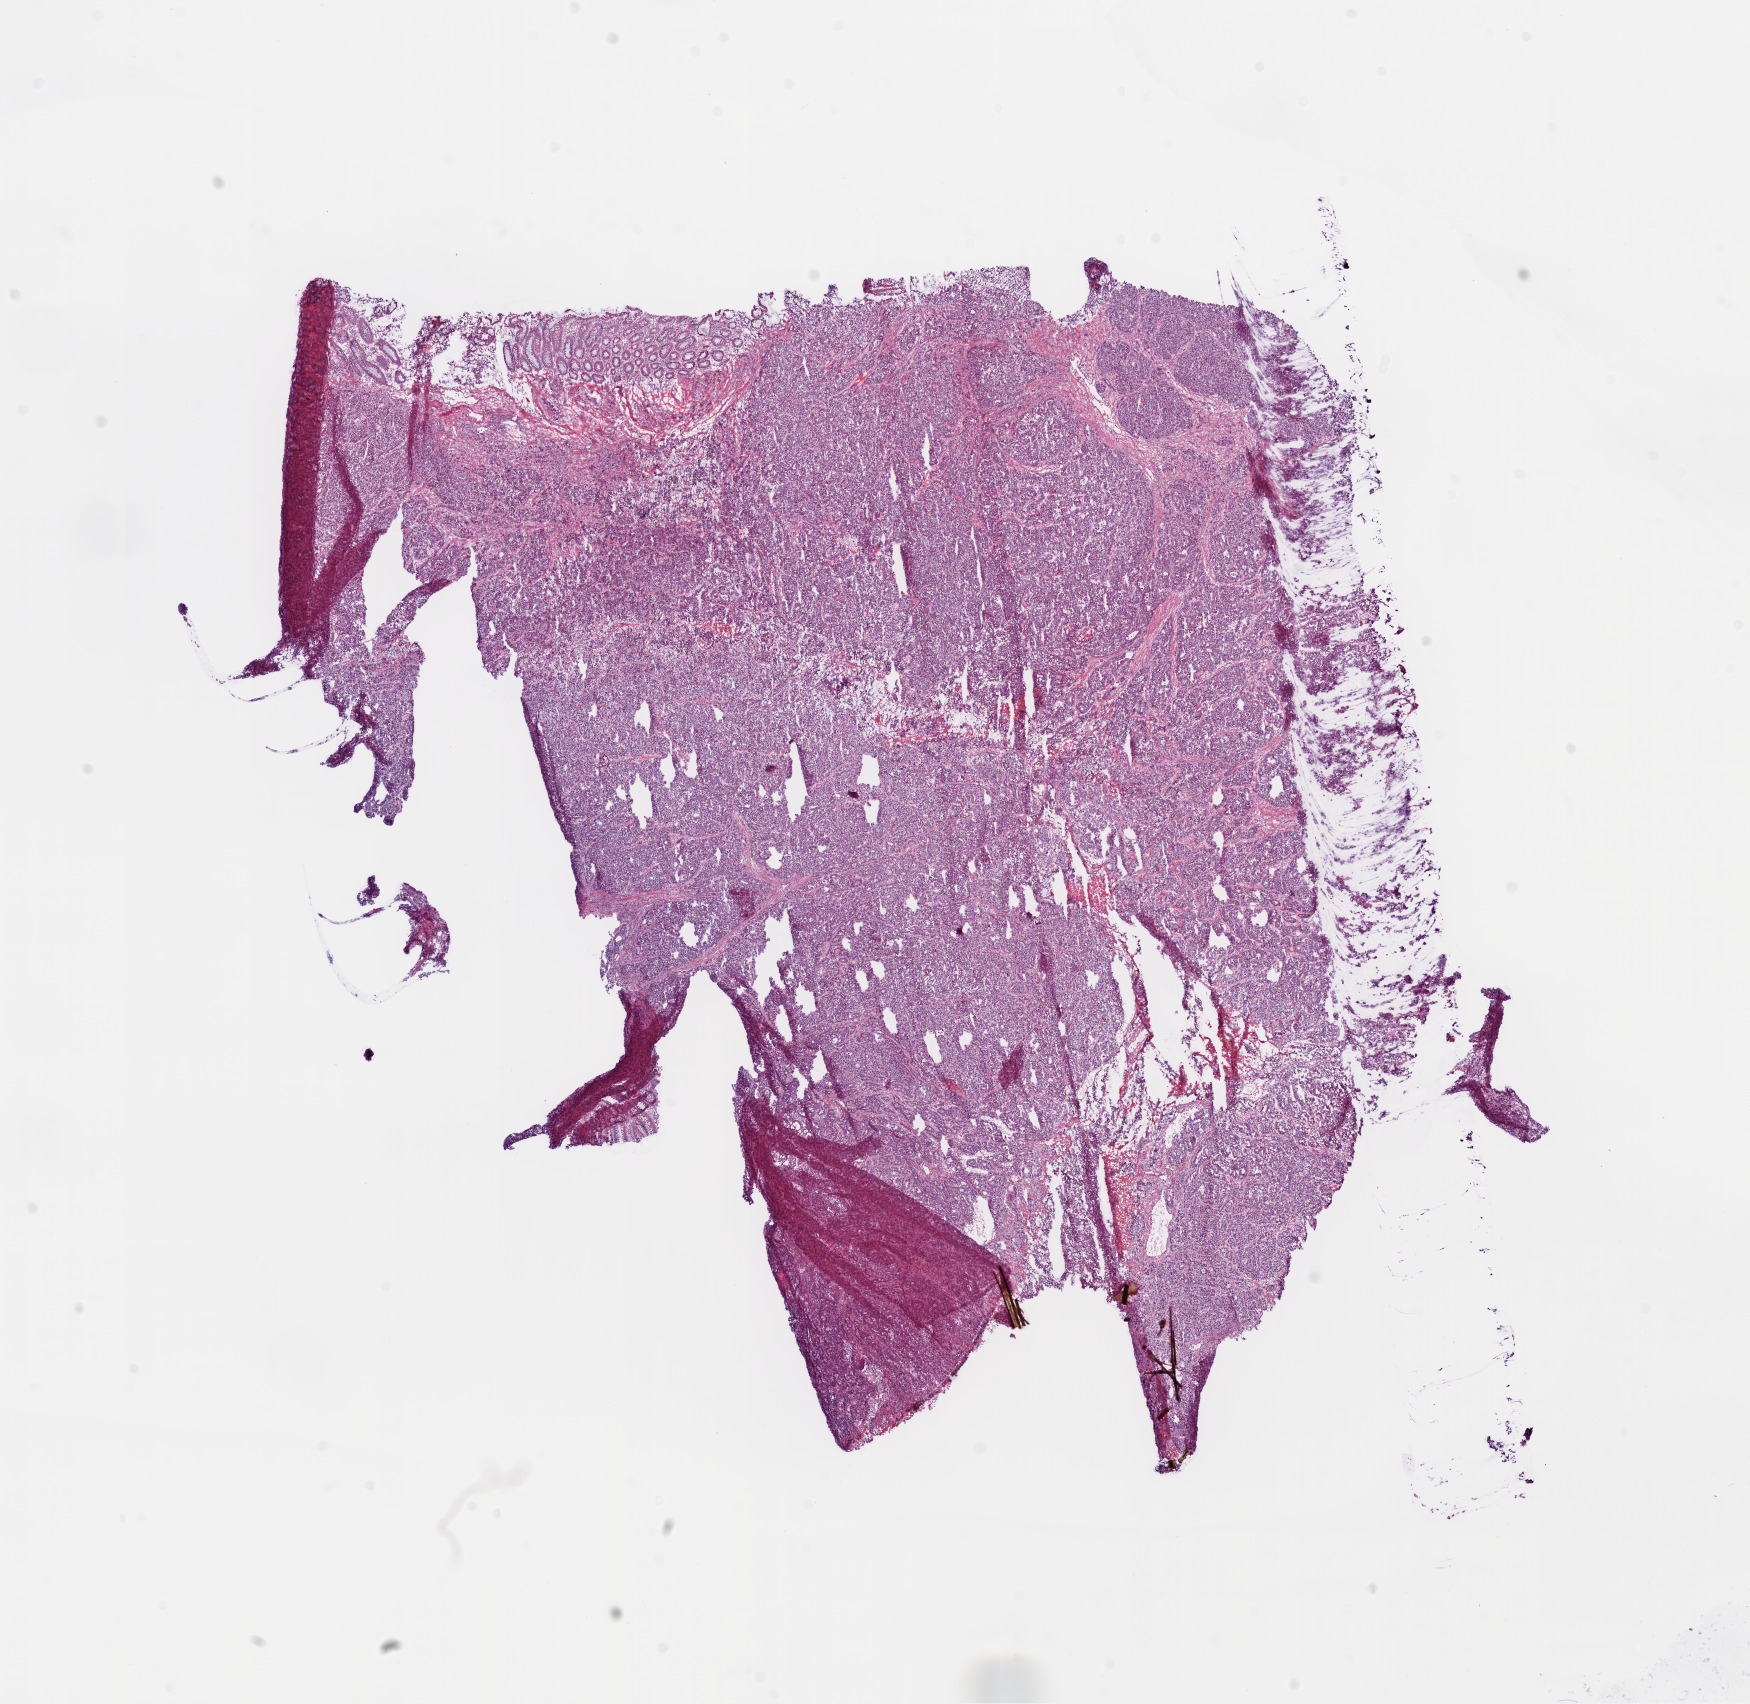
Whole-slide histology image, H&E — whole scanned area (about 14.0 x 13.7 mm, from a 20x scan) shown as a low-resolution overview, frozen section from the bottom of the tissue portion, colon, primary tumour sample. Female patient; age at initial diagnosis 84 years. Slide review estimates, as recorded: tumour nuclei 85%, normal cells 5%, stromal cells 5%, necrosis 5%.
- histologic diagnosis: Adenocarcinoma with neuroendocrine differentiation
- AJCC pathologic stage: III